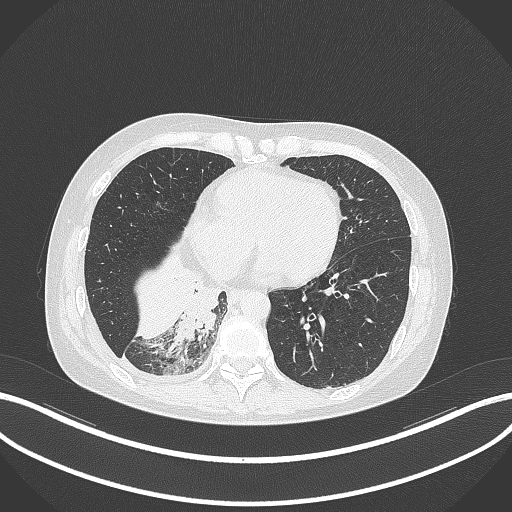
Chest CT, one axial slice. Slice 100 of 329 in the series (ordered by position). 120 kVp. Lung window (W 1500 / L -600 HU). 512 × 512 image matrix, field of view 400 × 400 mm. Female patient, age 63 years. Case-level facts recorded for this patient, not image findings: clinical TNM (as recorded): T1c N0 M0.
Annotated regions visible in this slice (bounding box drawn by a radiologist):
- lung tumour (recorded histology: adenocarcinoma): box from (x=175, y=286) to (x=221, y=343) px